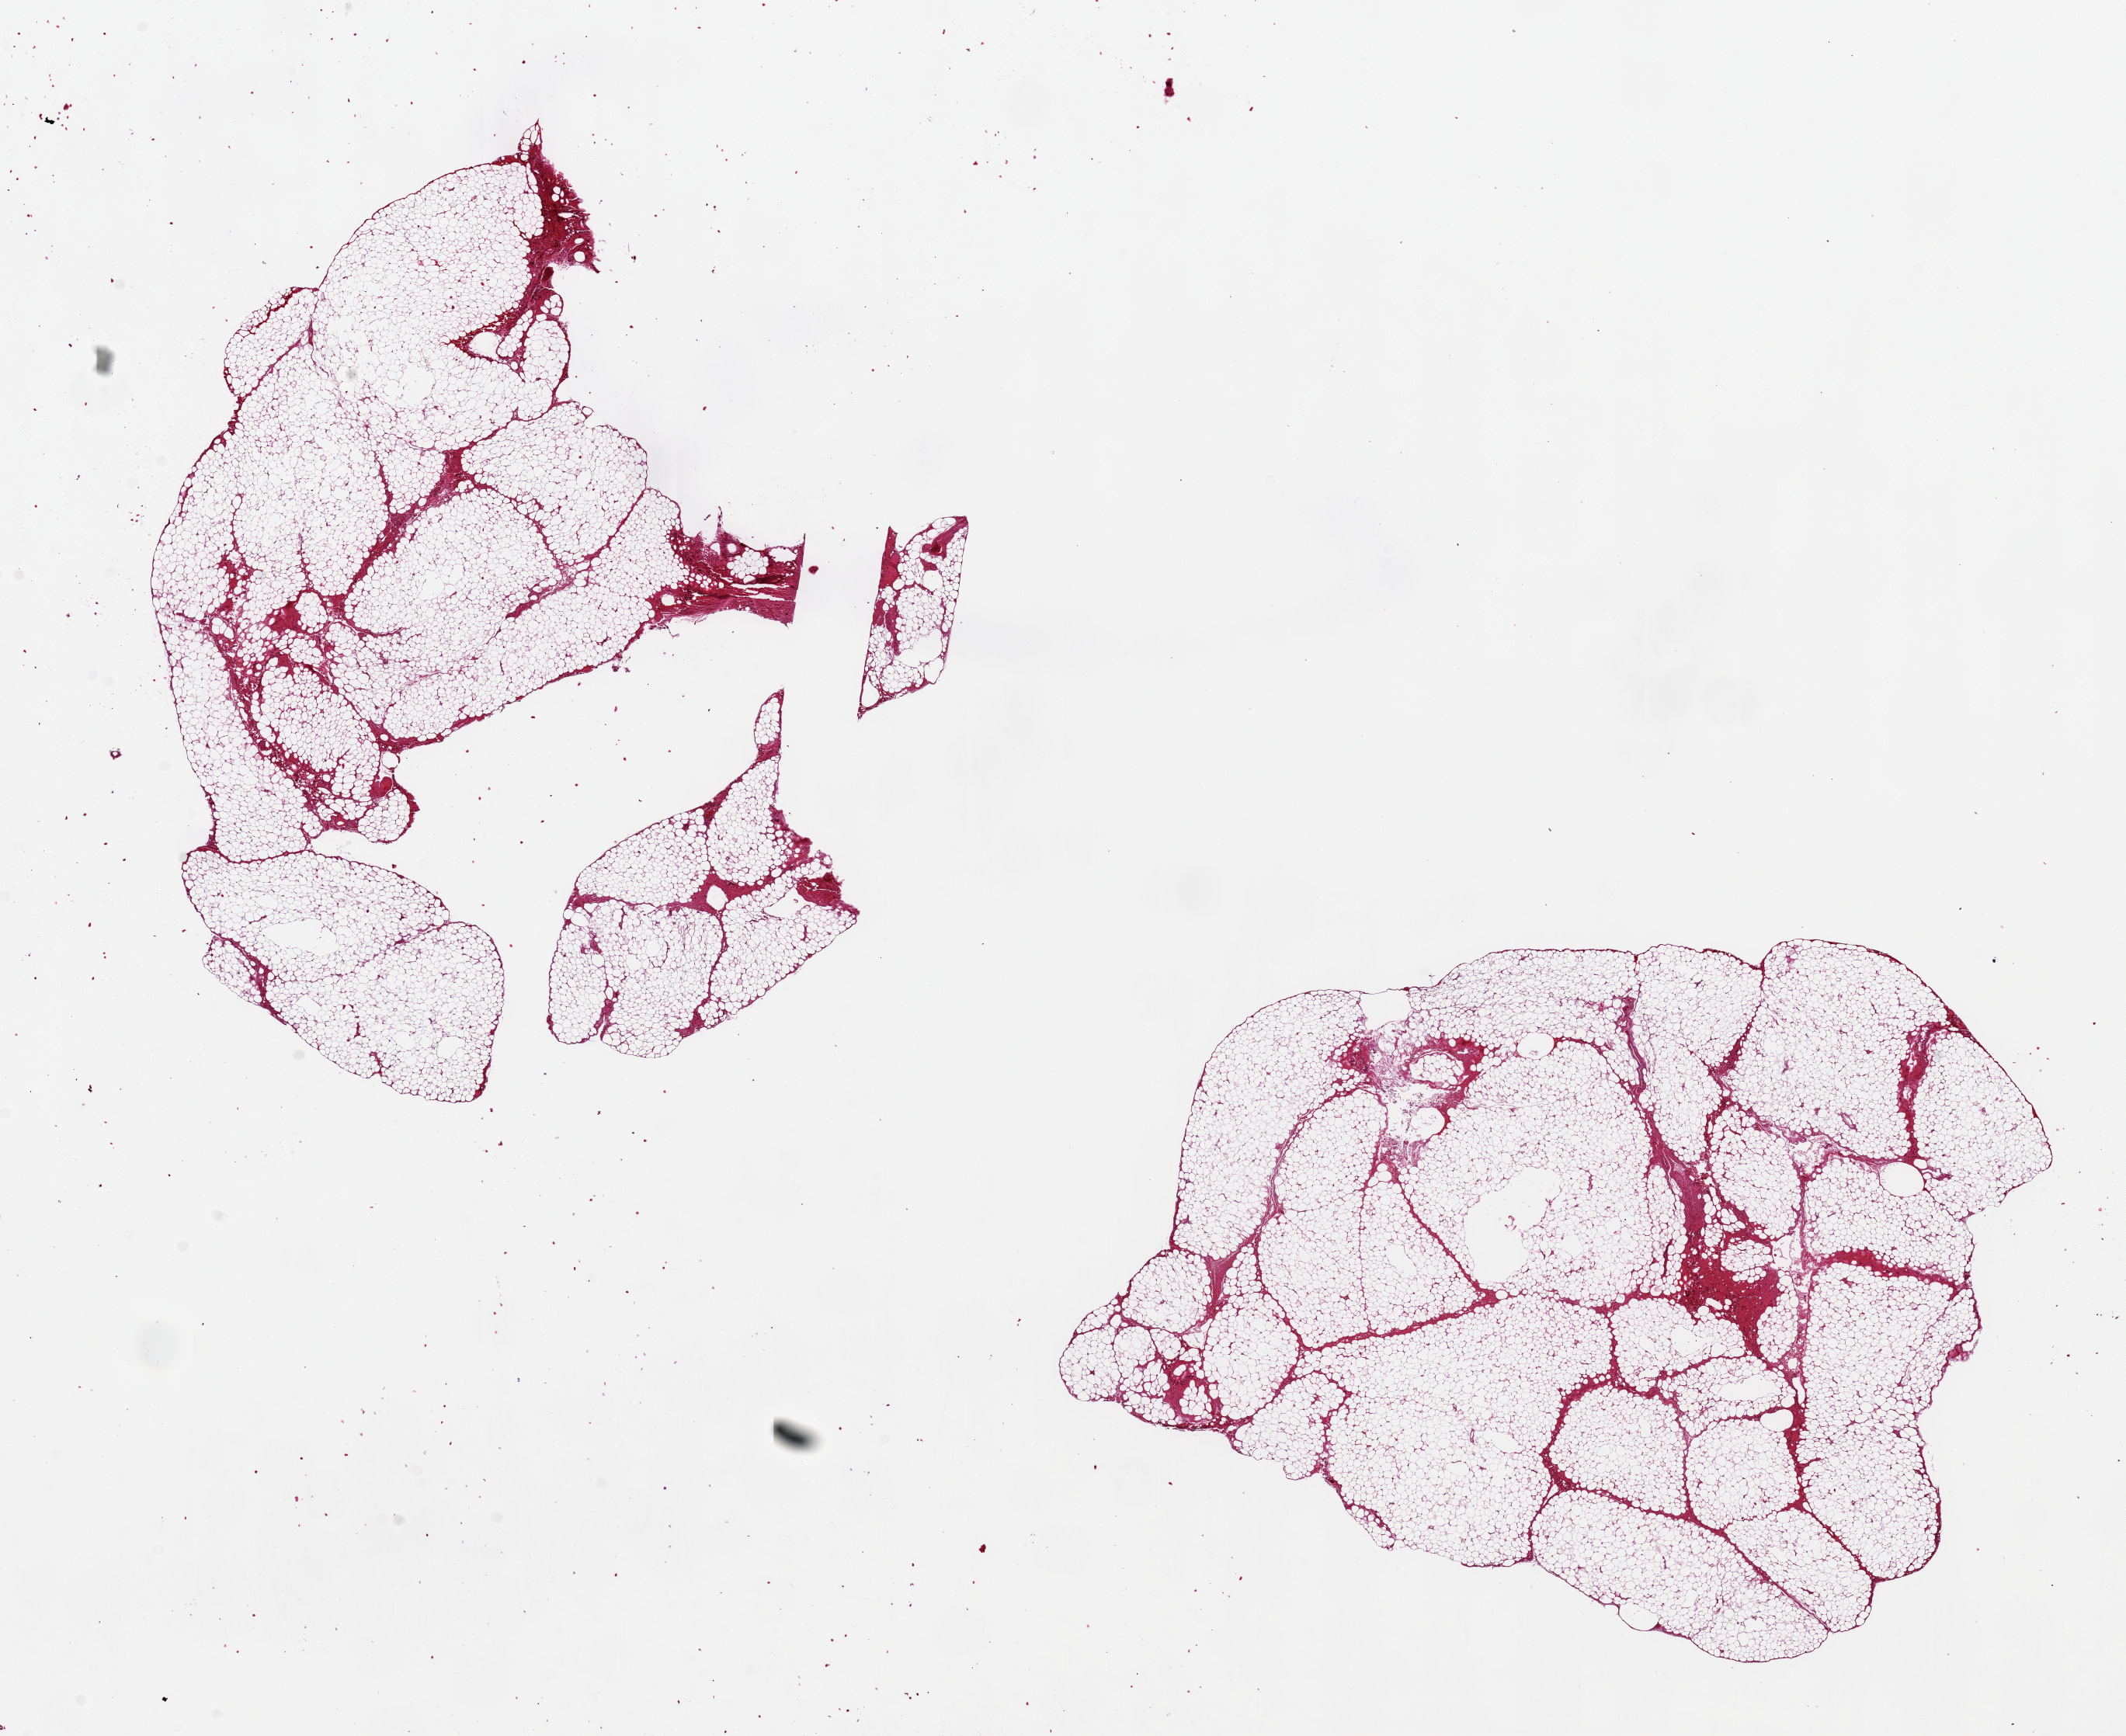
Whole-slide image, hematoxylin and eosin (H&E) stain, brightfield — whole scanned area (about 21.7 x 17.7 mm, from a 20x scan) shown as a low-resolution overview, PAXgene-fixed, paraffin-embedded tissue, sampled site (target tissue): omentum, tissue donor sample. Donor sex: male.
• reviewer comment on this tissue sample: 2 pieces, 10x8 & 9x7mm; No artifacts